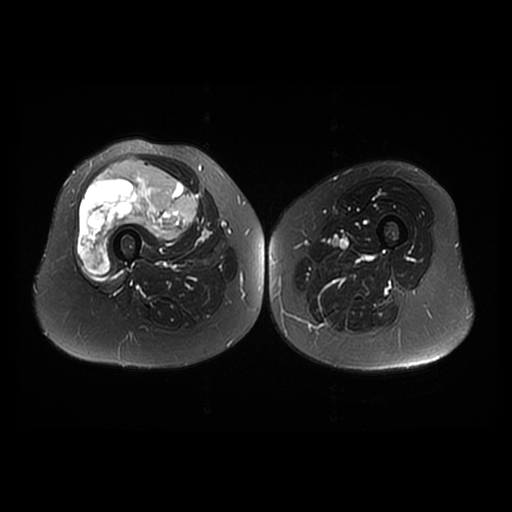
MRI of an extremity soft-tissue mass, one axial slice; position 19 of 42 along the scan axis; T2-weighted fat-saturated; 6 mm slice thickness; 512 × 512 image matrix. Female patient. From the clinical record (not read from this slice): histological type: pleiomorphic undifferentiated sarcoma; grade: high; site of the primary tumour: right quadricep.
Structures marked on this image (outlined manually by an expert reader):
- gross tumour volume including surrounding oedema: bounding box [x1, y1, x2, y2] px = [78, 159, 197, 274]
- gross tumour volume (mass): [78, 159, 197, 274]